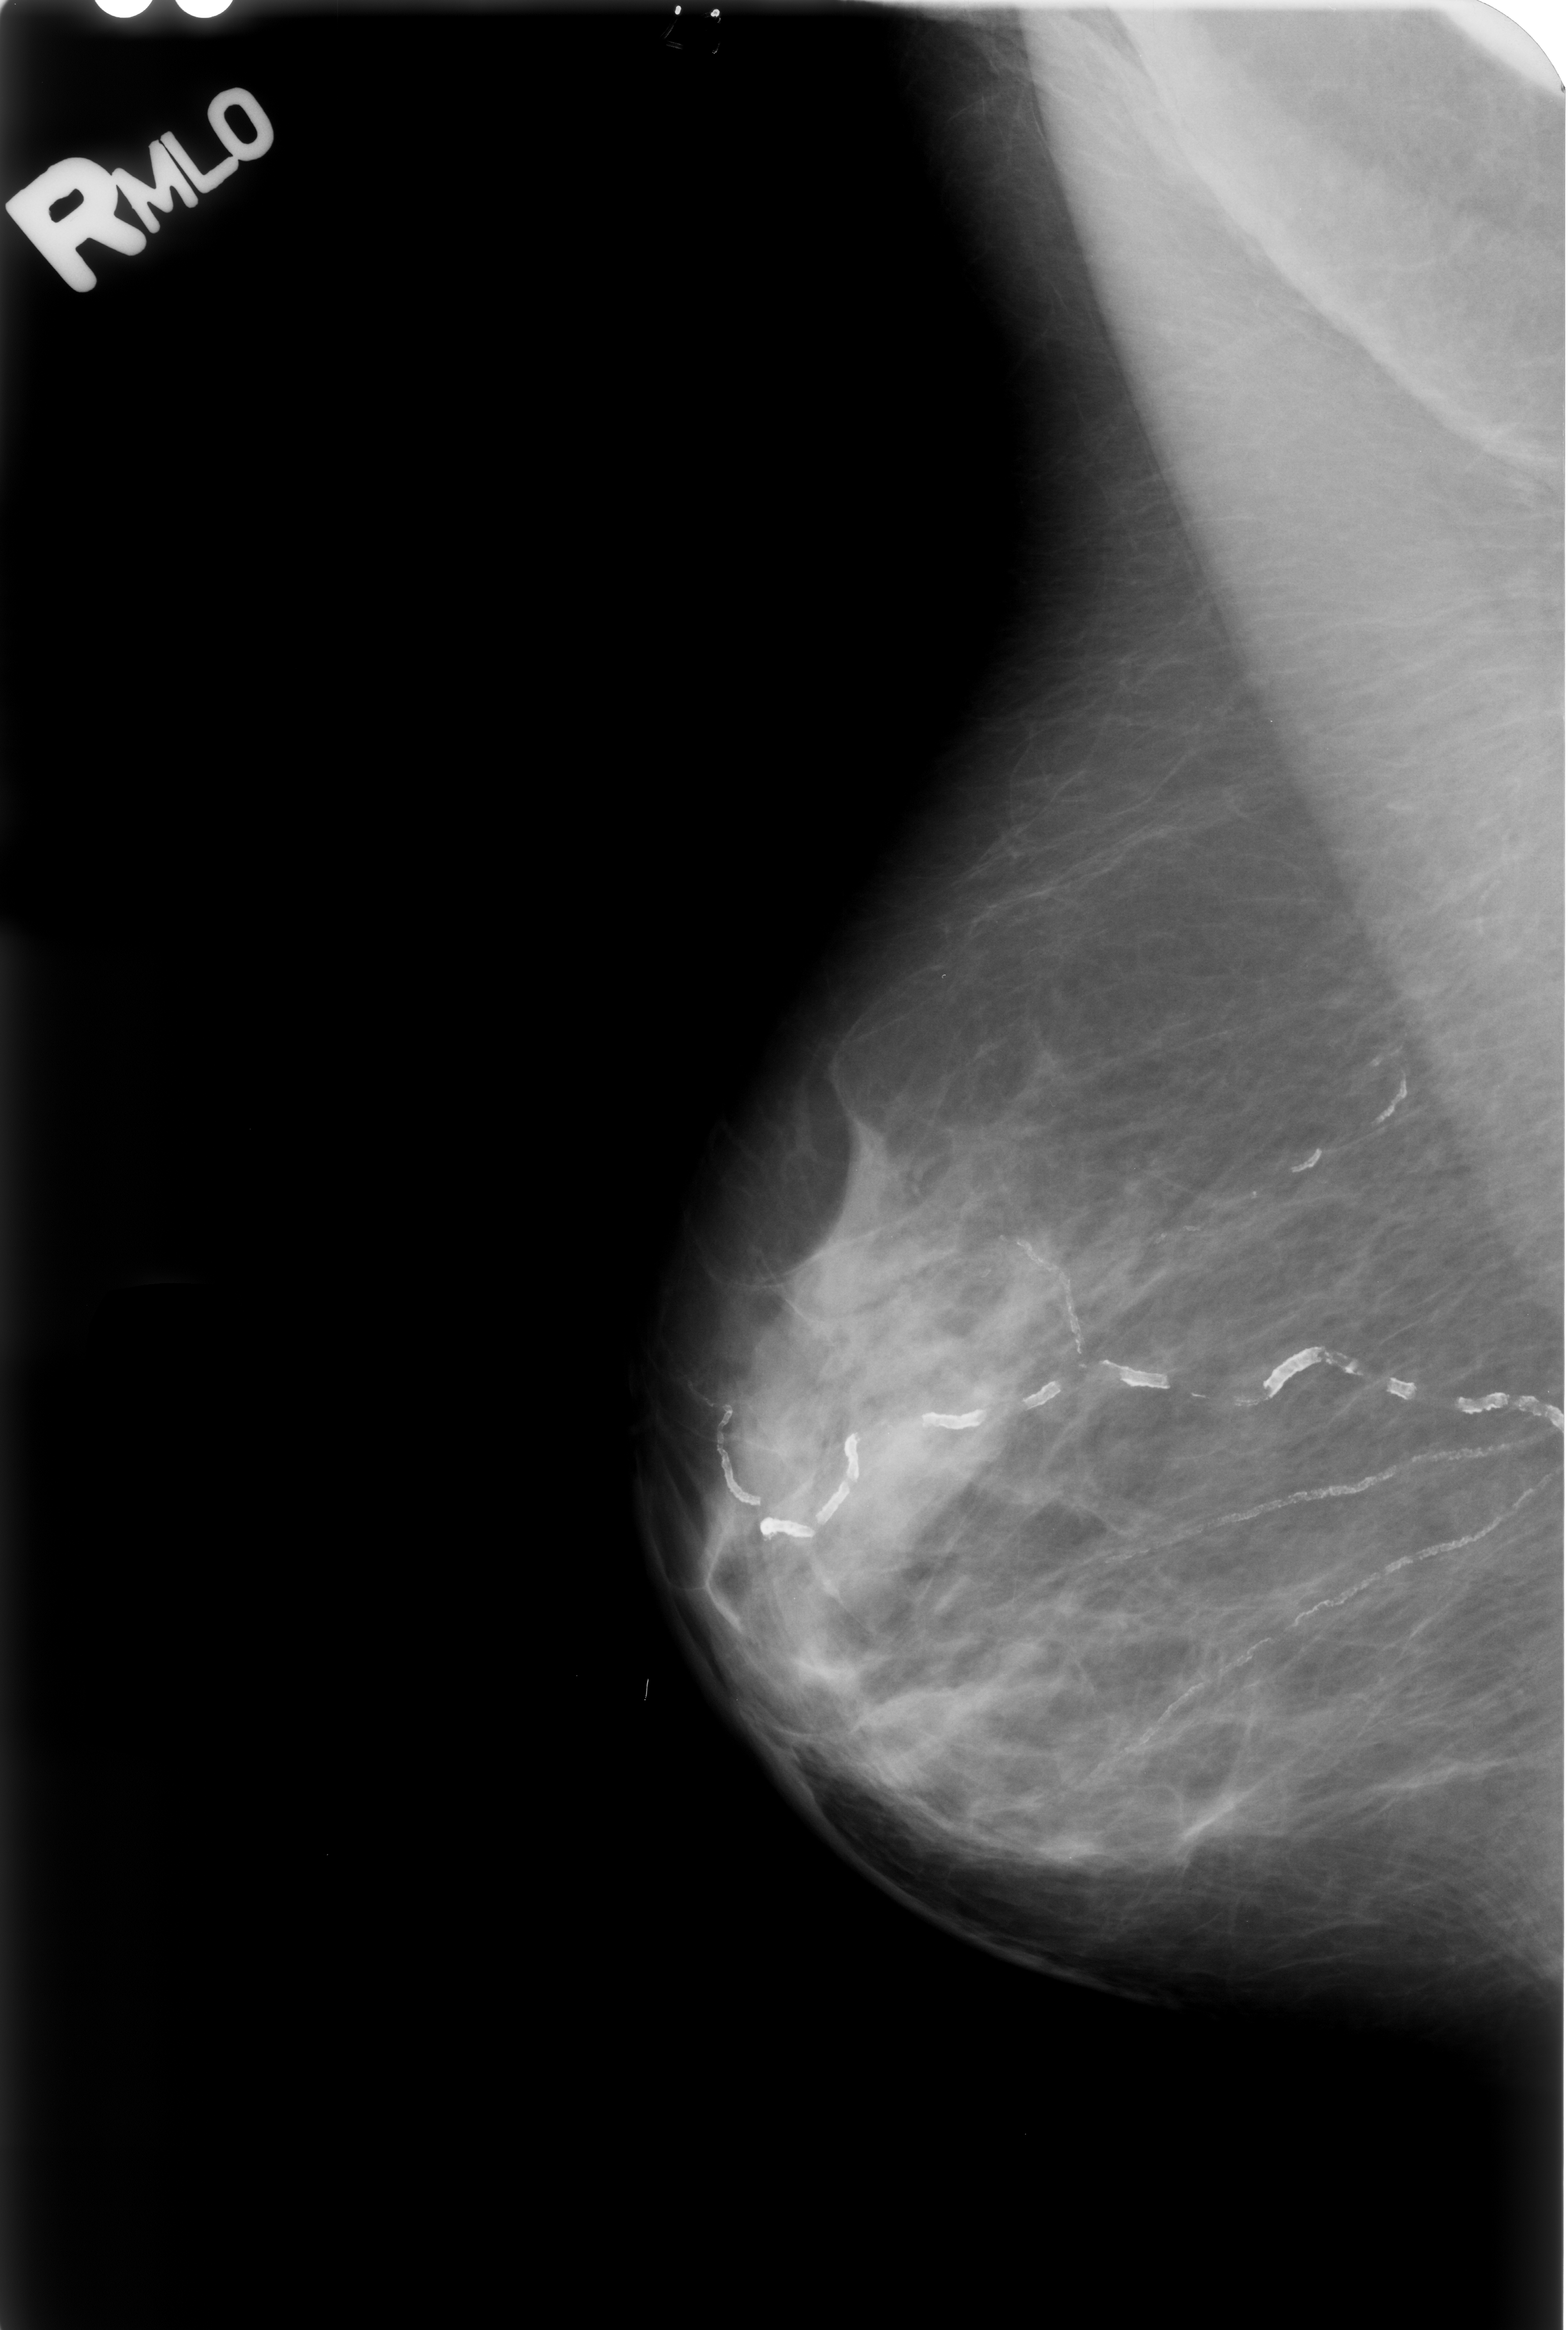
Mammogram (digitized film). Right breast. Mediolateral oblique (MLO) view. BI-RADS breast density category 2 (scale 1–4). 1568 × 2330 image matrix.
Expert-marked regions of interest on this image (one box per marked abnormality):
- calcifications, morphology vascular; BI-RADS assessment category 2; subtlety rating 5 on a 1 (subtle) to 5 (obvious) scale; outcome (as recorded, no biopsy): benign without callback (not worked up further): bounding box [x1, y1, x2, y2] px = [704, 1344, 1557, 1557]